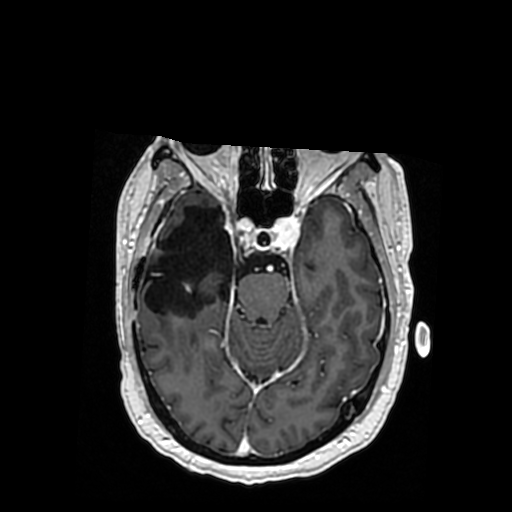
Brain MRI from a brain-tumour surgery series, one axial slice; slice 225 of 364 in the series (ordered by position); T1-weighted post-contrast; 0.5 mm slice thickness; 512 × 512 image matrix, field of view 260 × 260 mm. Case-level facts recorded for this patient, not image findings: histopathology: Oligodendroglioma; WHO grade: 3; IDH mutation: yes.
Annotated regions visible in this slice (outlined manually by an expert reader):
- previous resection cavity: bounding box [x1, y1, x2, y2] px = [143, 206, 233, 317]